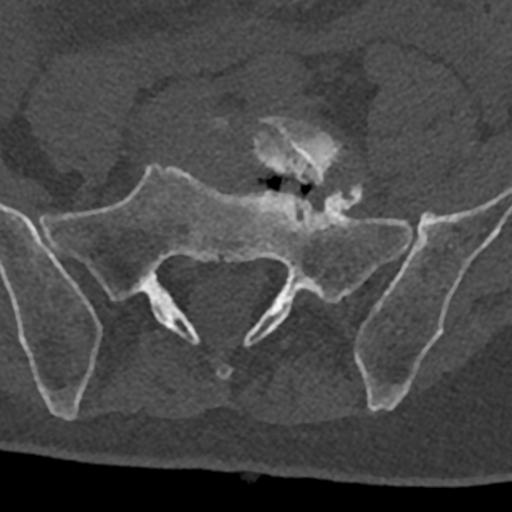
CT including the spine, one axial slice; position 155 of 797 along the scan axis; reconstruction kernel Br40s/3; 120 kVp; bone window (W 1800 / L 400 HU); 0.5 mm slice thickness; 512 × 512 image matrix, field of view 160 × 160 mm. Male patient, age 74 years. From the clinical record (not read from this slice): primary cancer: renal.
Outlined on this slice (semi-automatically segmented with operator editing):
- L5 vertebra: bounding box [x1, y1, x2, y2] px = [215, 116, 347, 187]